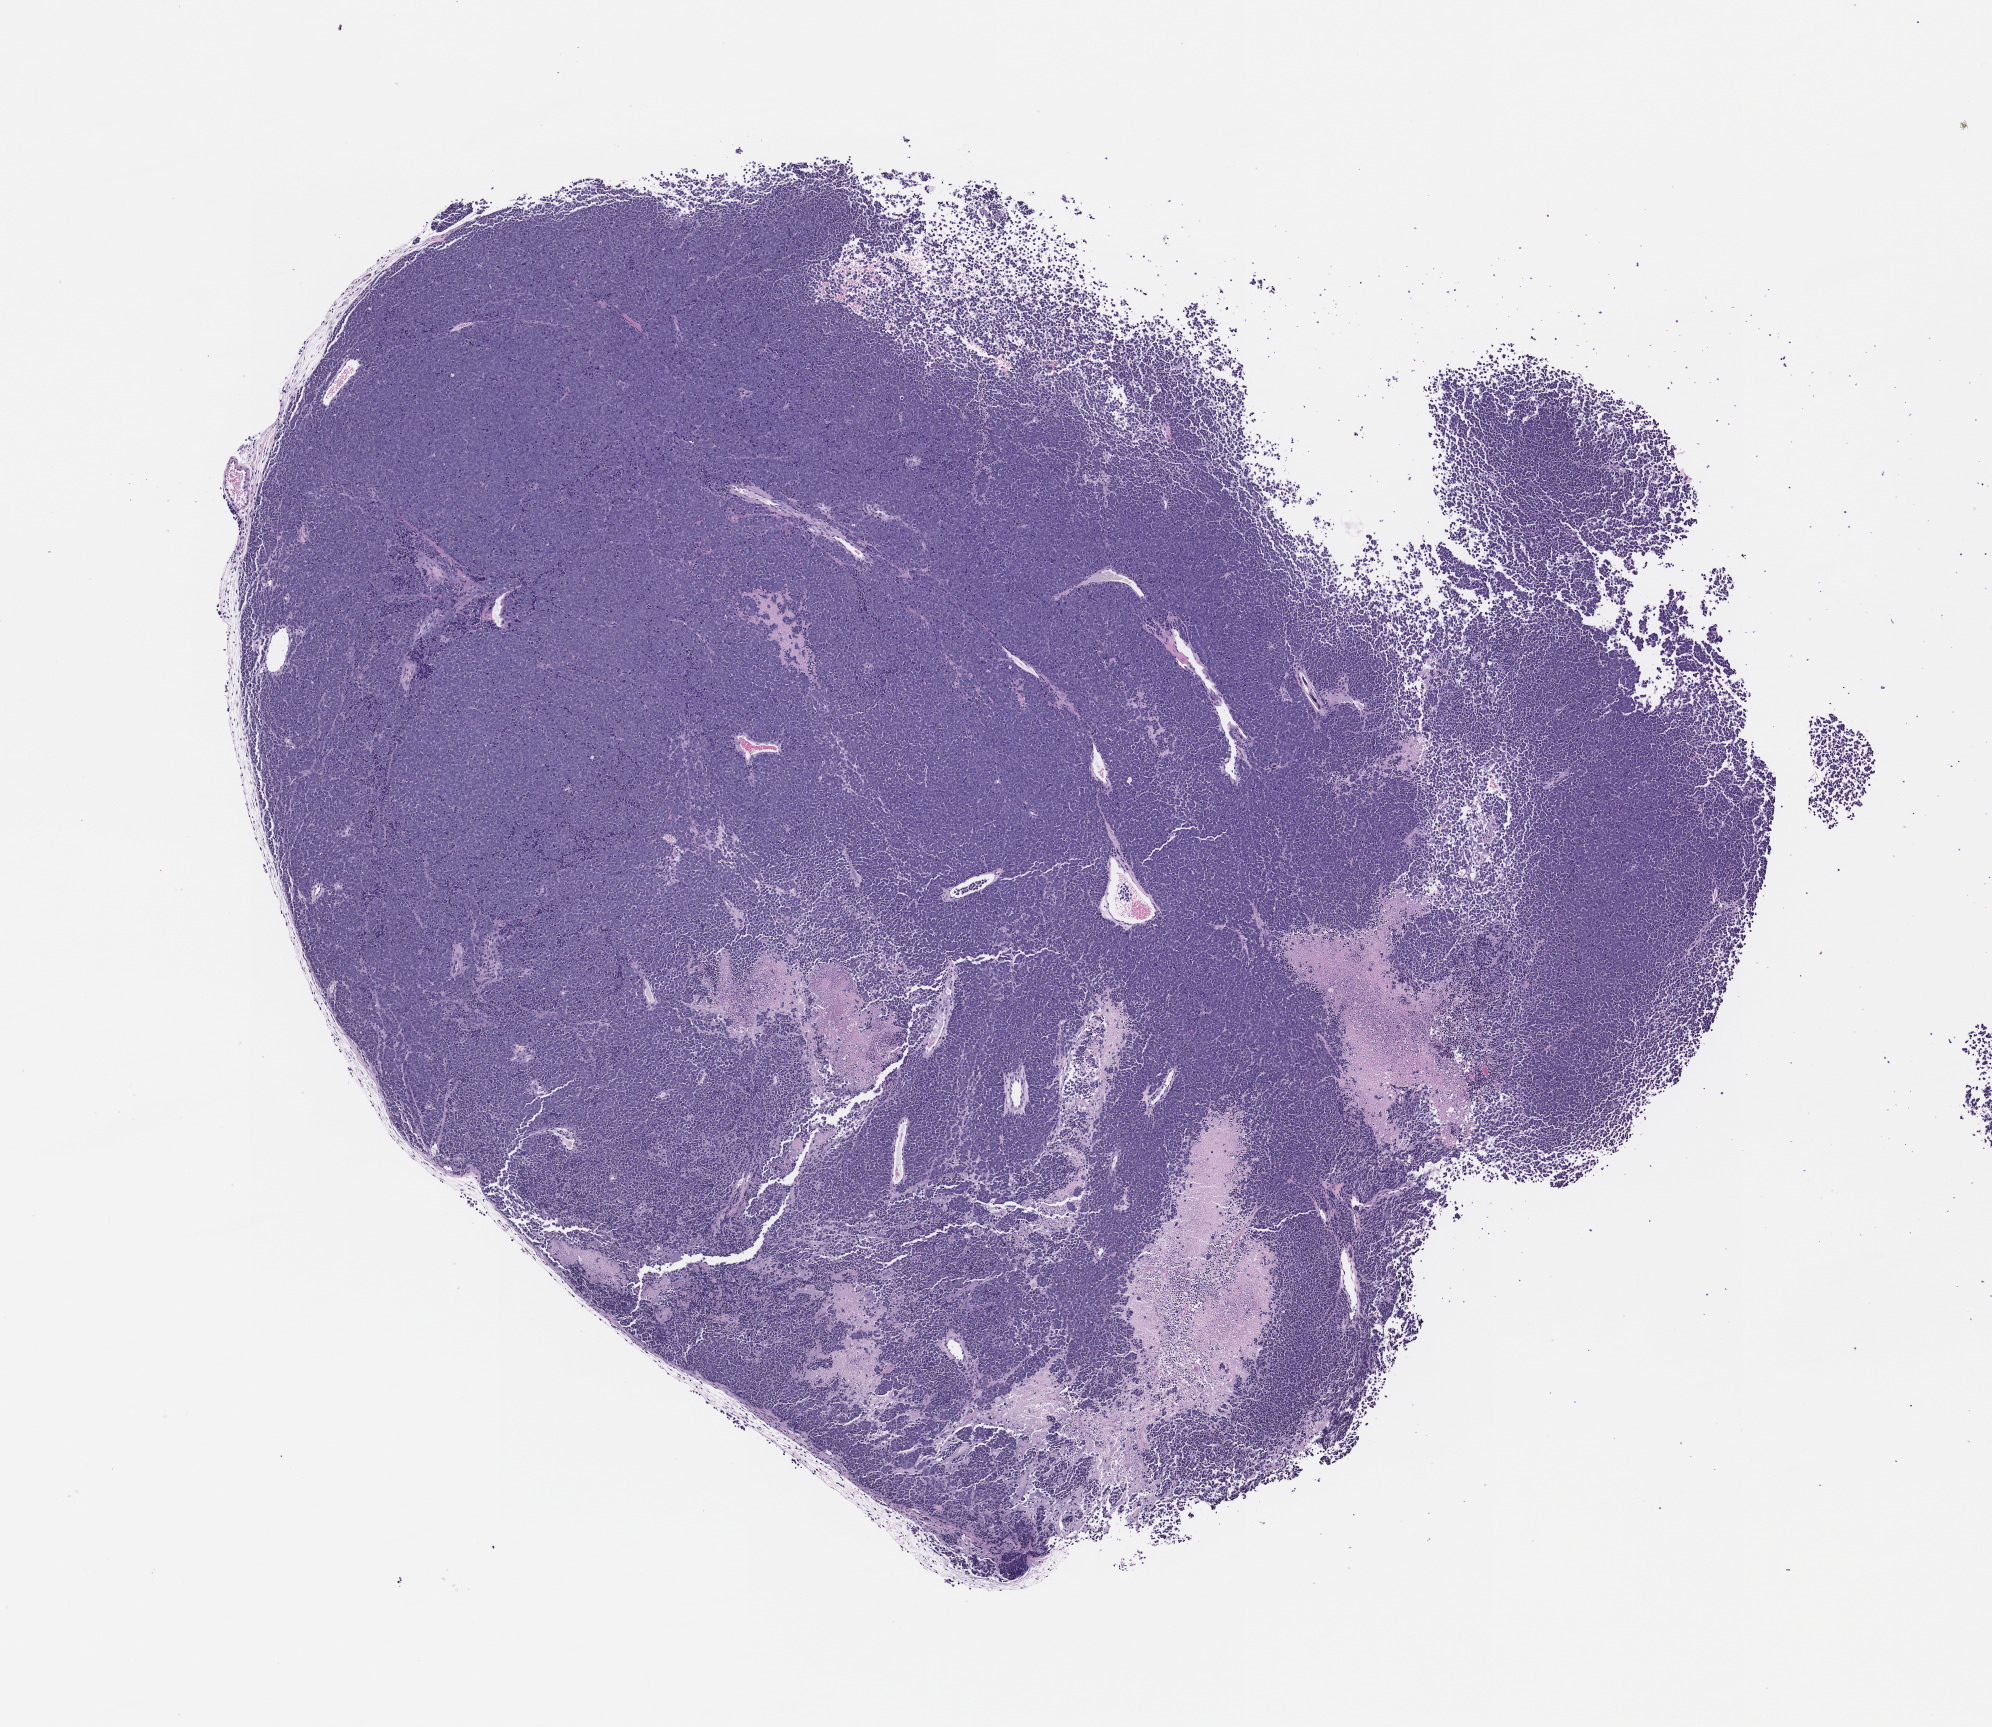
H&E whole-slide image of a patient-derived xenograft (PDX) tumor grown in a mouse, passage 1 — whole scanned area (about 8.0 x 6.9 mm) shown as a low-resolution overview; formalin-fixed paraffin-embedded section; tumor site category: endocrine.
Originating patient diagnosis: Merkel Cell Carcinoma.